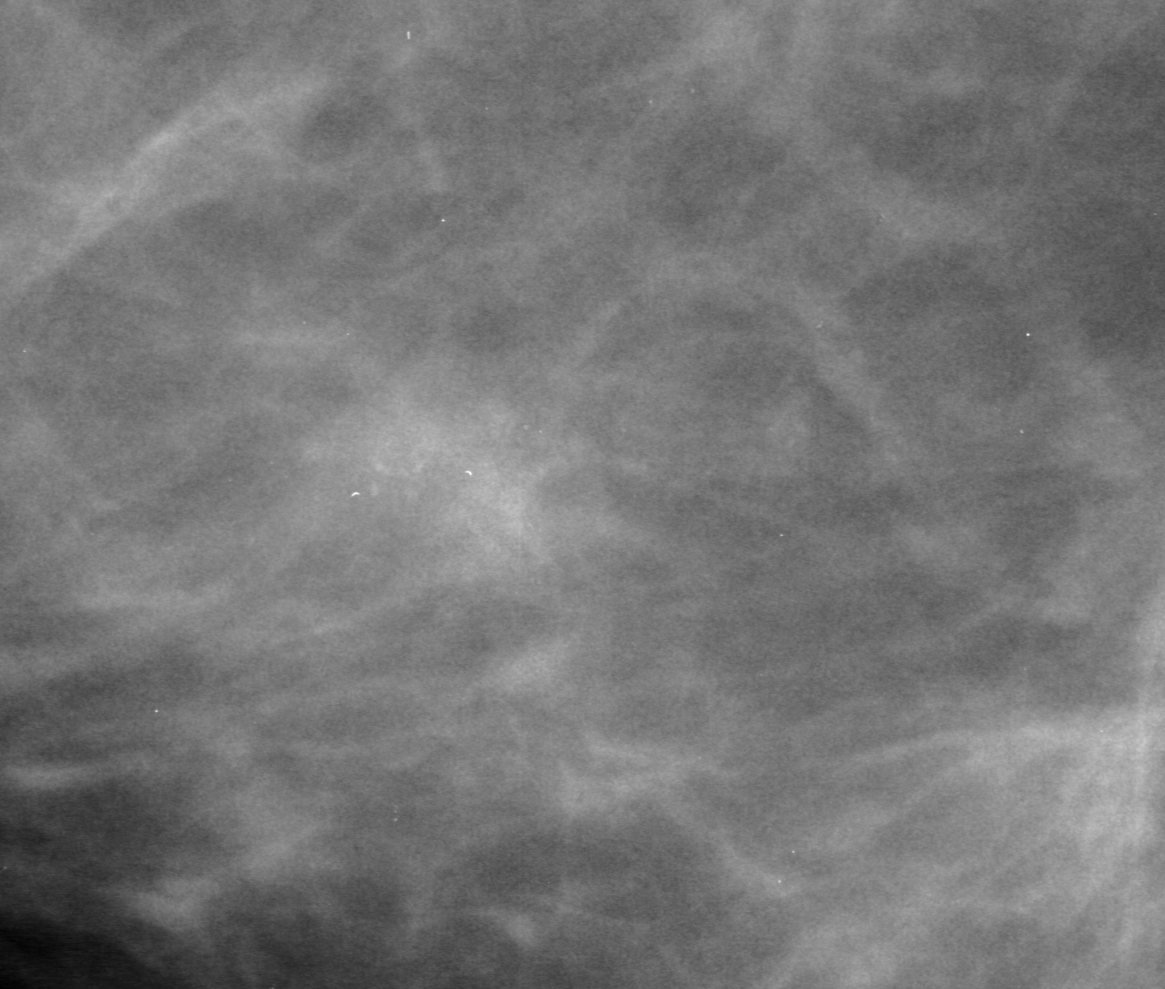
Cropped region of a digitized screen-film mammogram centred on a radiologist-marked abnormality; right breast; MLO view; BI-RADS breast density category 2 (scale 1–4).
Calcifications, morphology pleomorphic, distribution clustered; BI-RADS assessment category 0 (incomplete: needs additional imaging); subtlety rating 2 on a 1 (subtle) to 5 (obvious) scale; pathology result (as recorded, not read from the image): malignant.